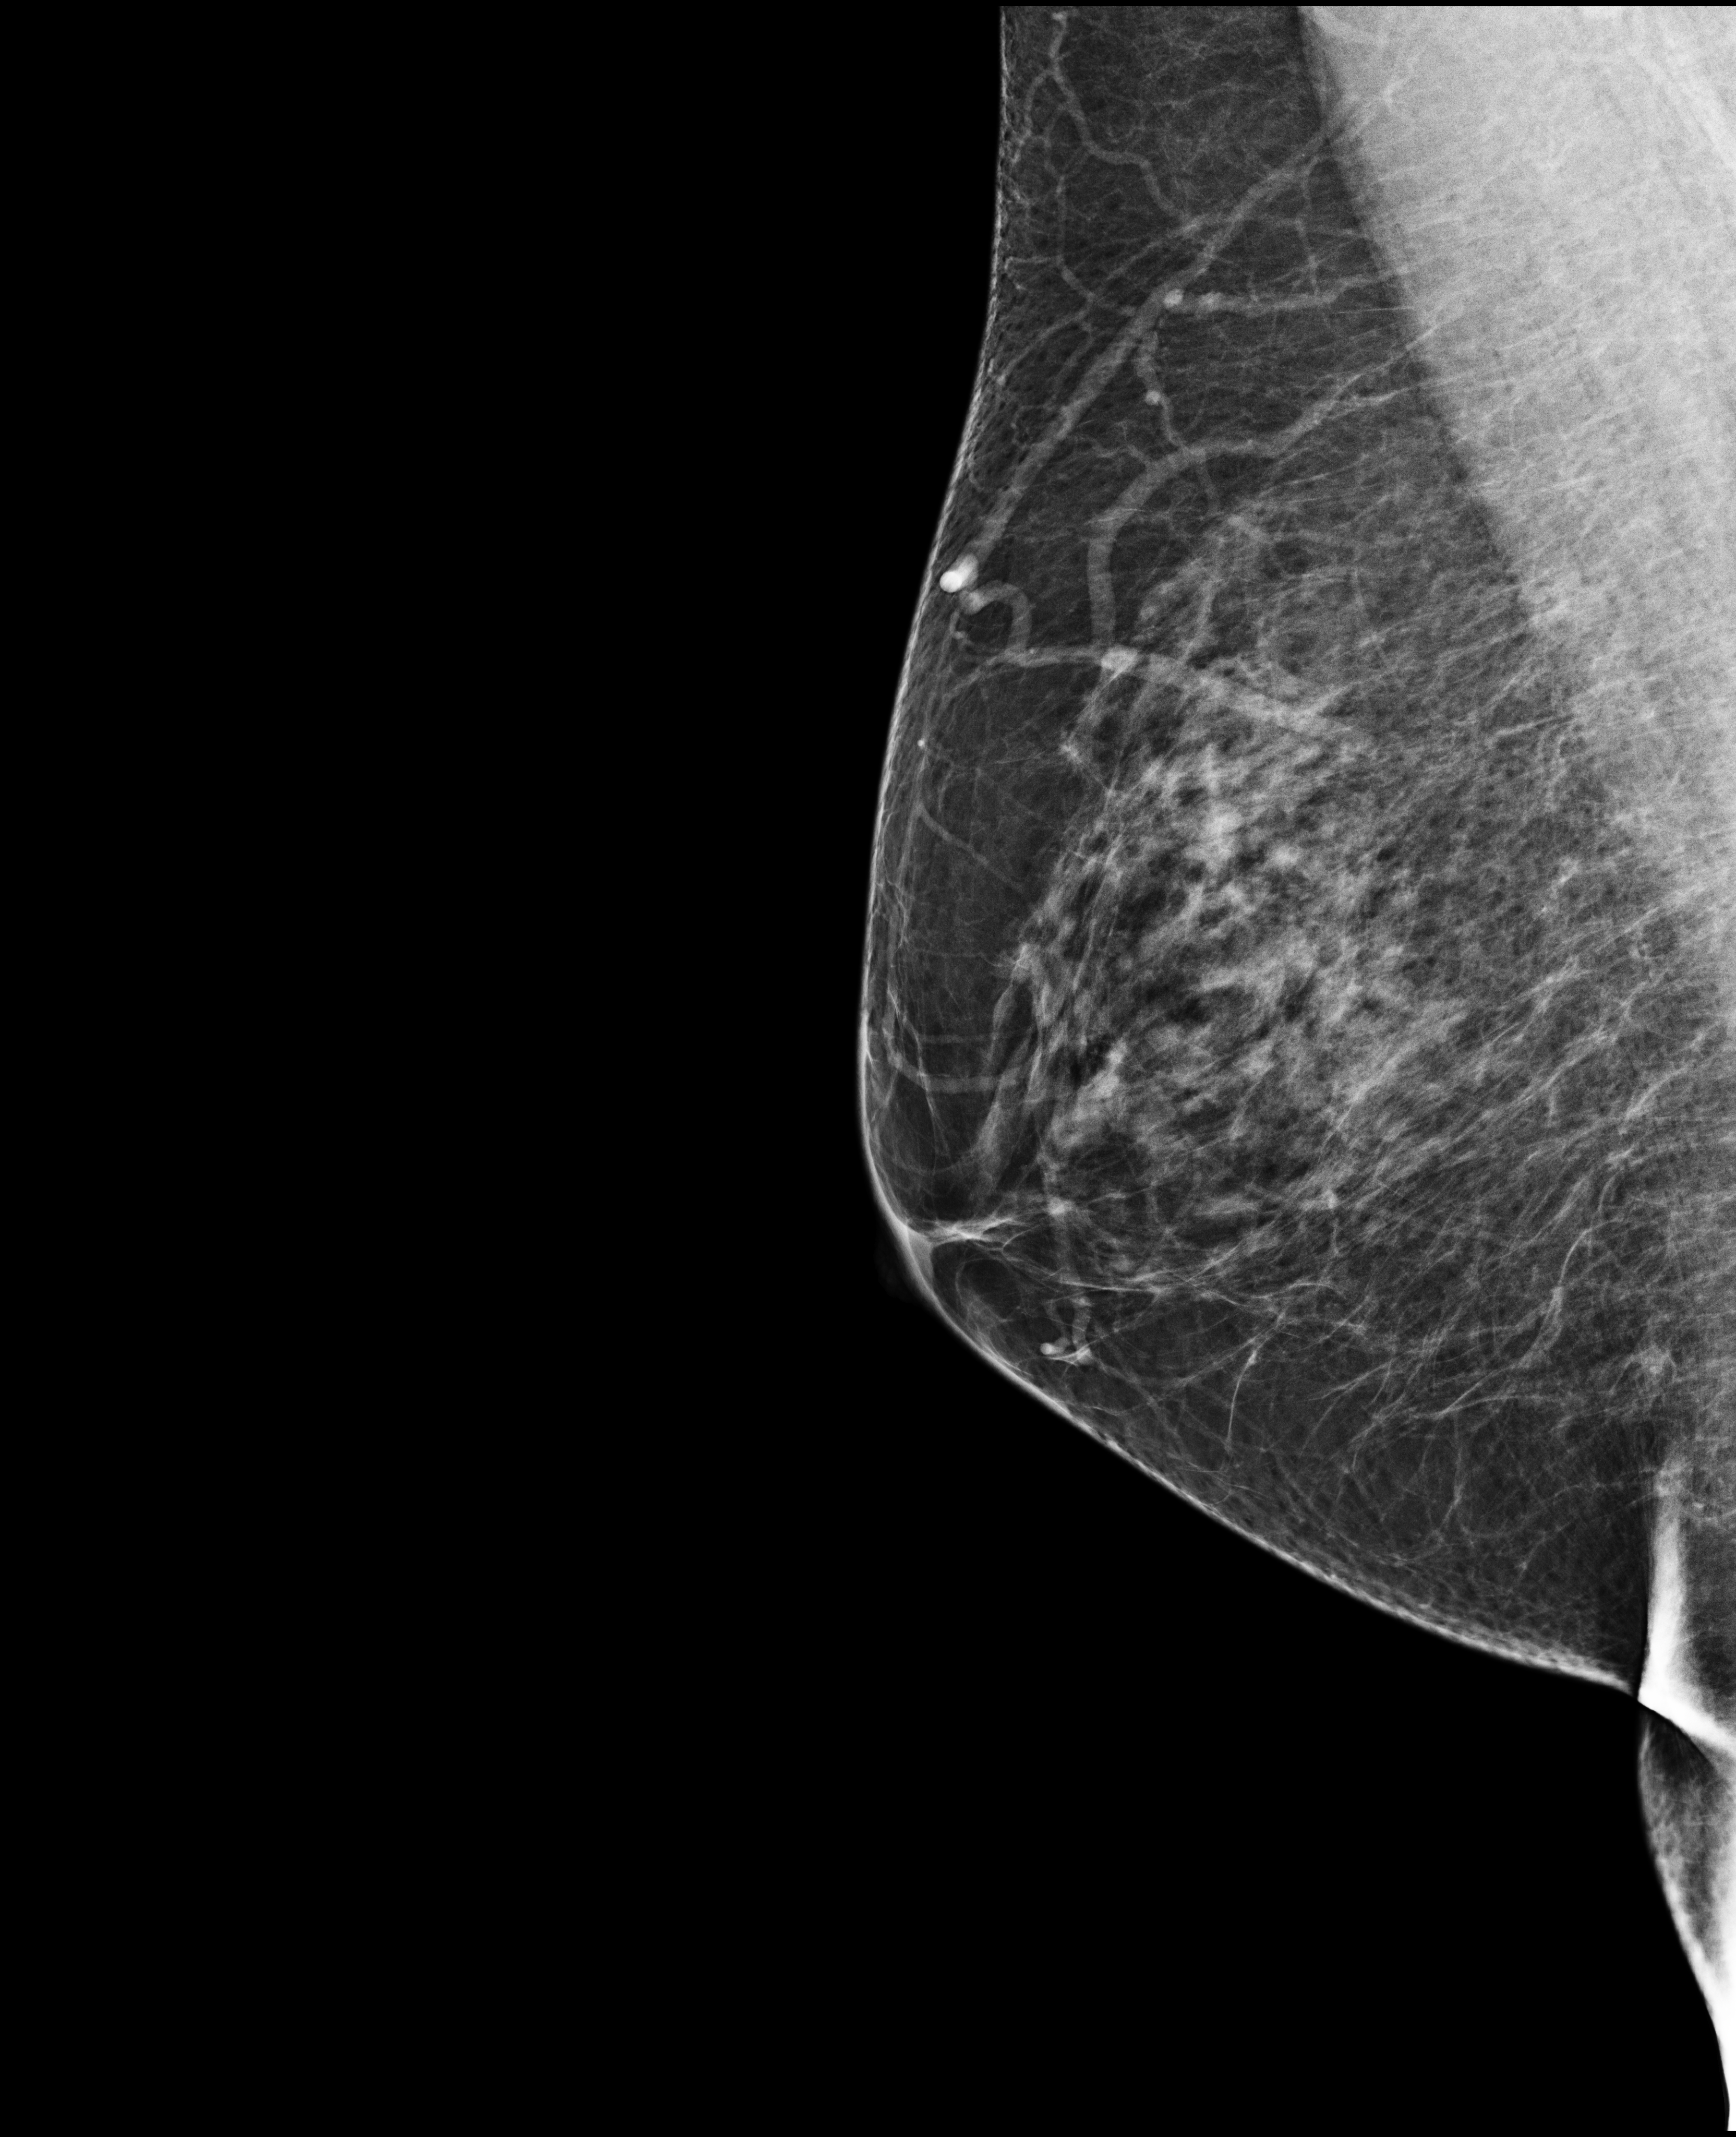
Screening examination; compressed breast thickness 62 mm. Patient aged 57 years (female).
Image type: full-field digital mammogram. Breast: right. Projection: MLO view.